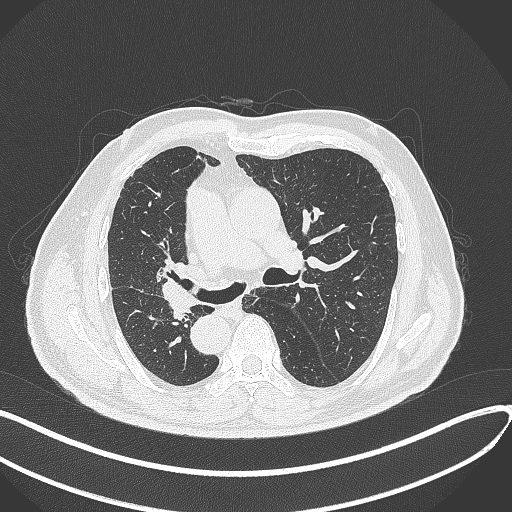
Chest CT, one axial slice. Slice 172 of 300 in the series (ordered by position). Reconstruction kernel B70f. 120 kVp. Lung window (W 1500 / L -600 HU). 1 mm slice thickness. 512 × 512 image matrix, field of view 400 × 400 mm. Male patient, age 67 years. From the clinical record (not read from this slice): clinical TNM (as recorded): T2a N0 M0.
Outlined on this slice (bounding box drawn by a radiologist):
- lung tumour (recorded histology: squamous cell carcinoma): bounding box (x1, y1, x2, y2) in pixels: (158, 271, 199, 326)